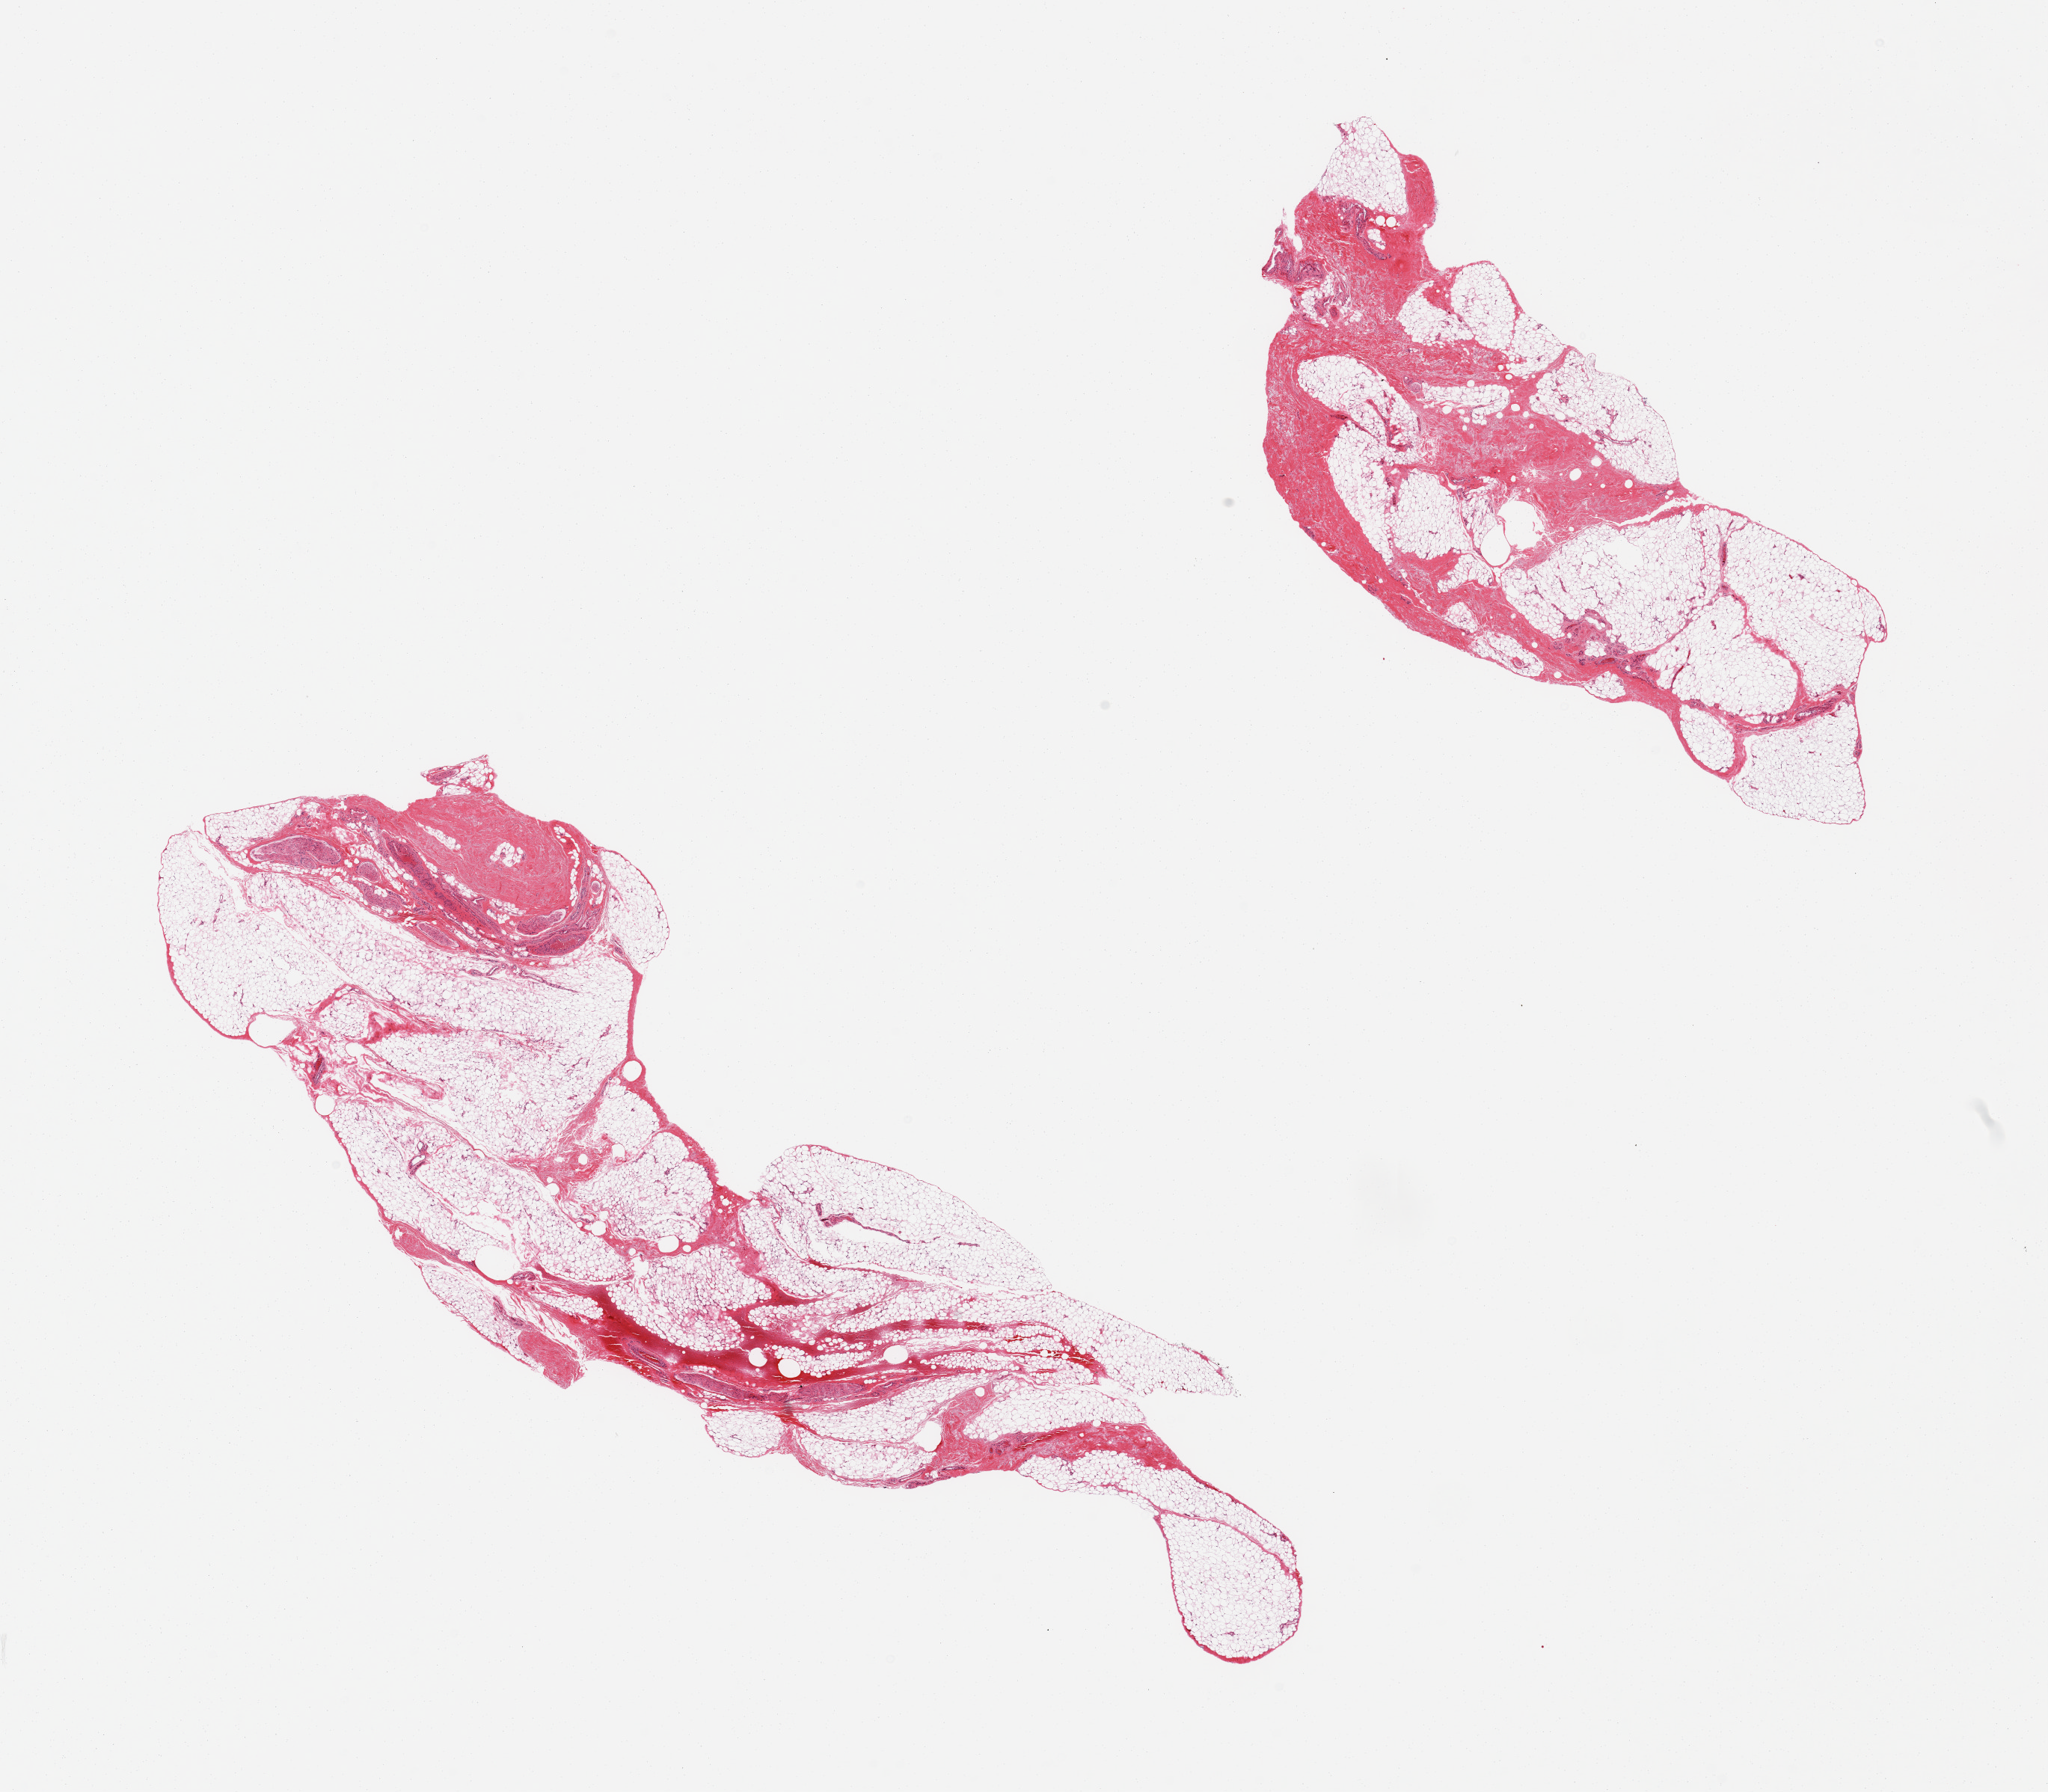
Haematoxylin and eosin whole-slide image, brightfield, a low-resolution overview of the entire scanned area, about 21.7 x 19.0 mm (slide scanned at 20x), PAXgene-fixed, paraffin-embedded tissue, target tissue: adipose tissue, donor tissue sample. Donor sex: male.
Reviewer comment on this tissue sample: 2 pieces, 20-30% is fibrous tissue, vessels, and nerve.